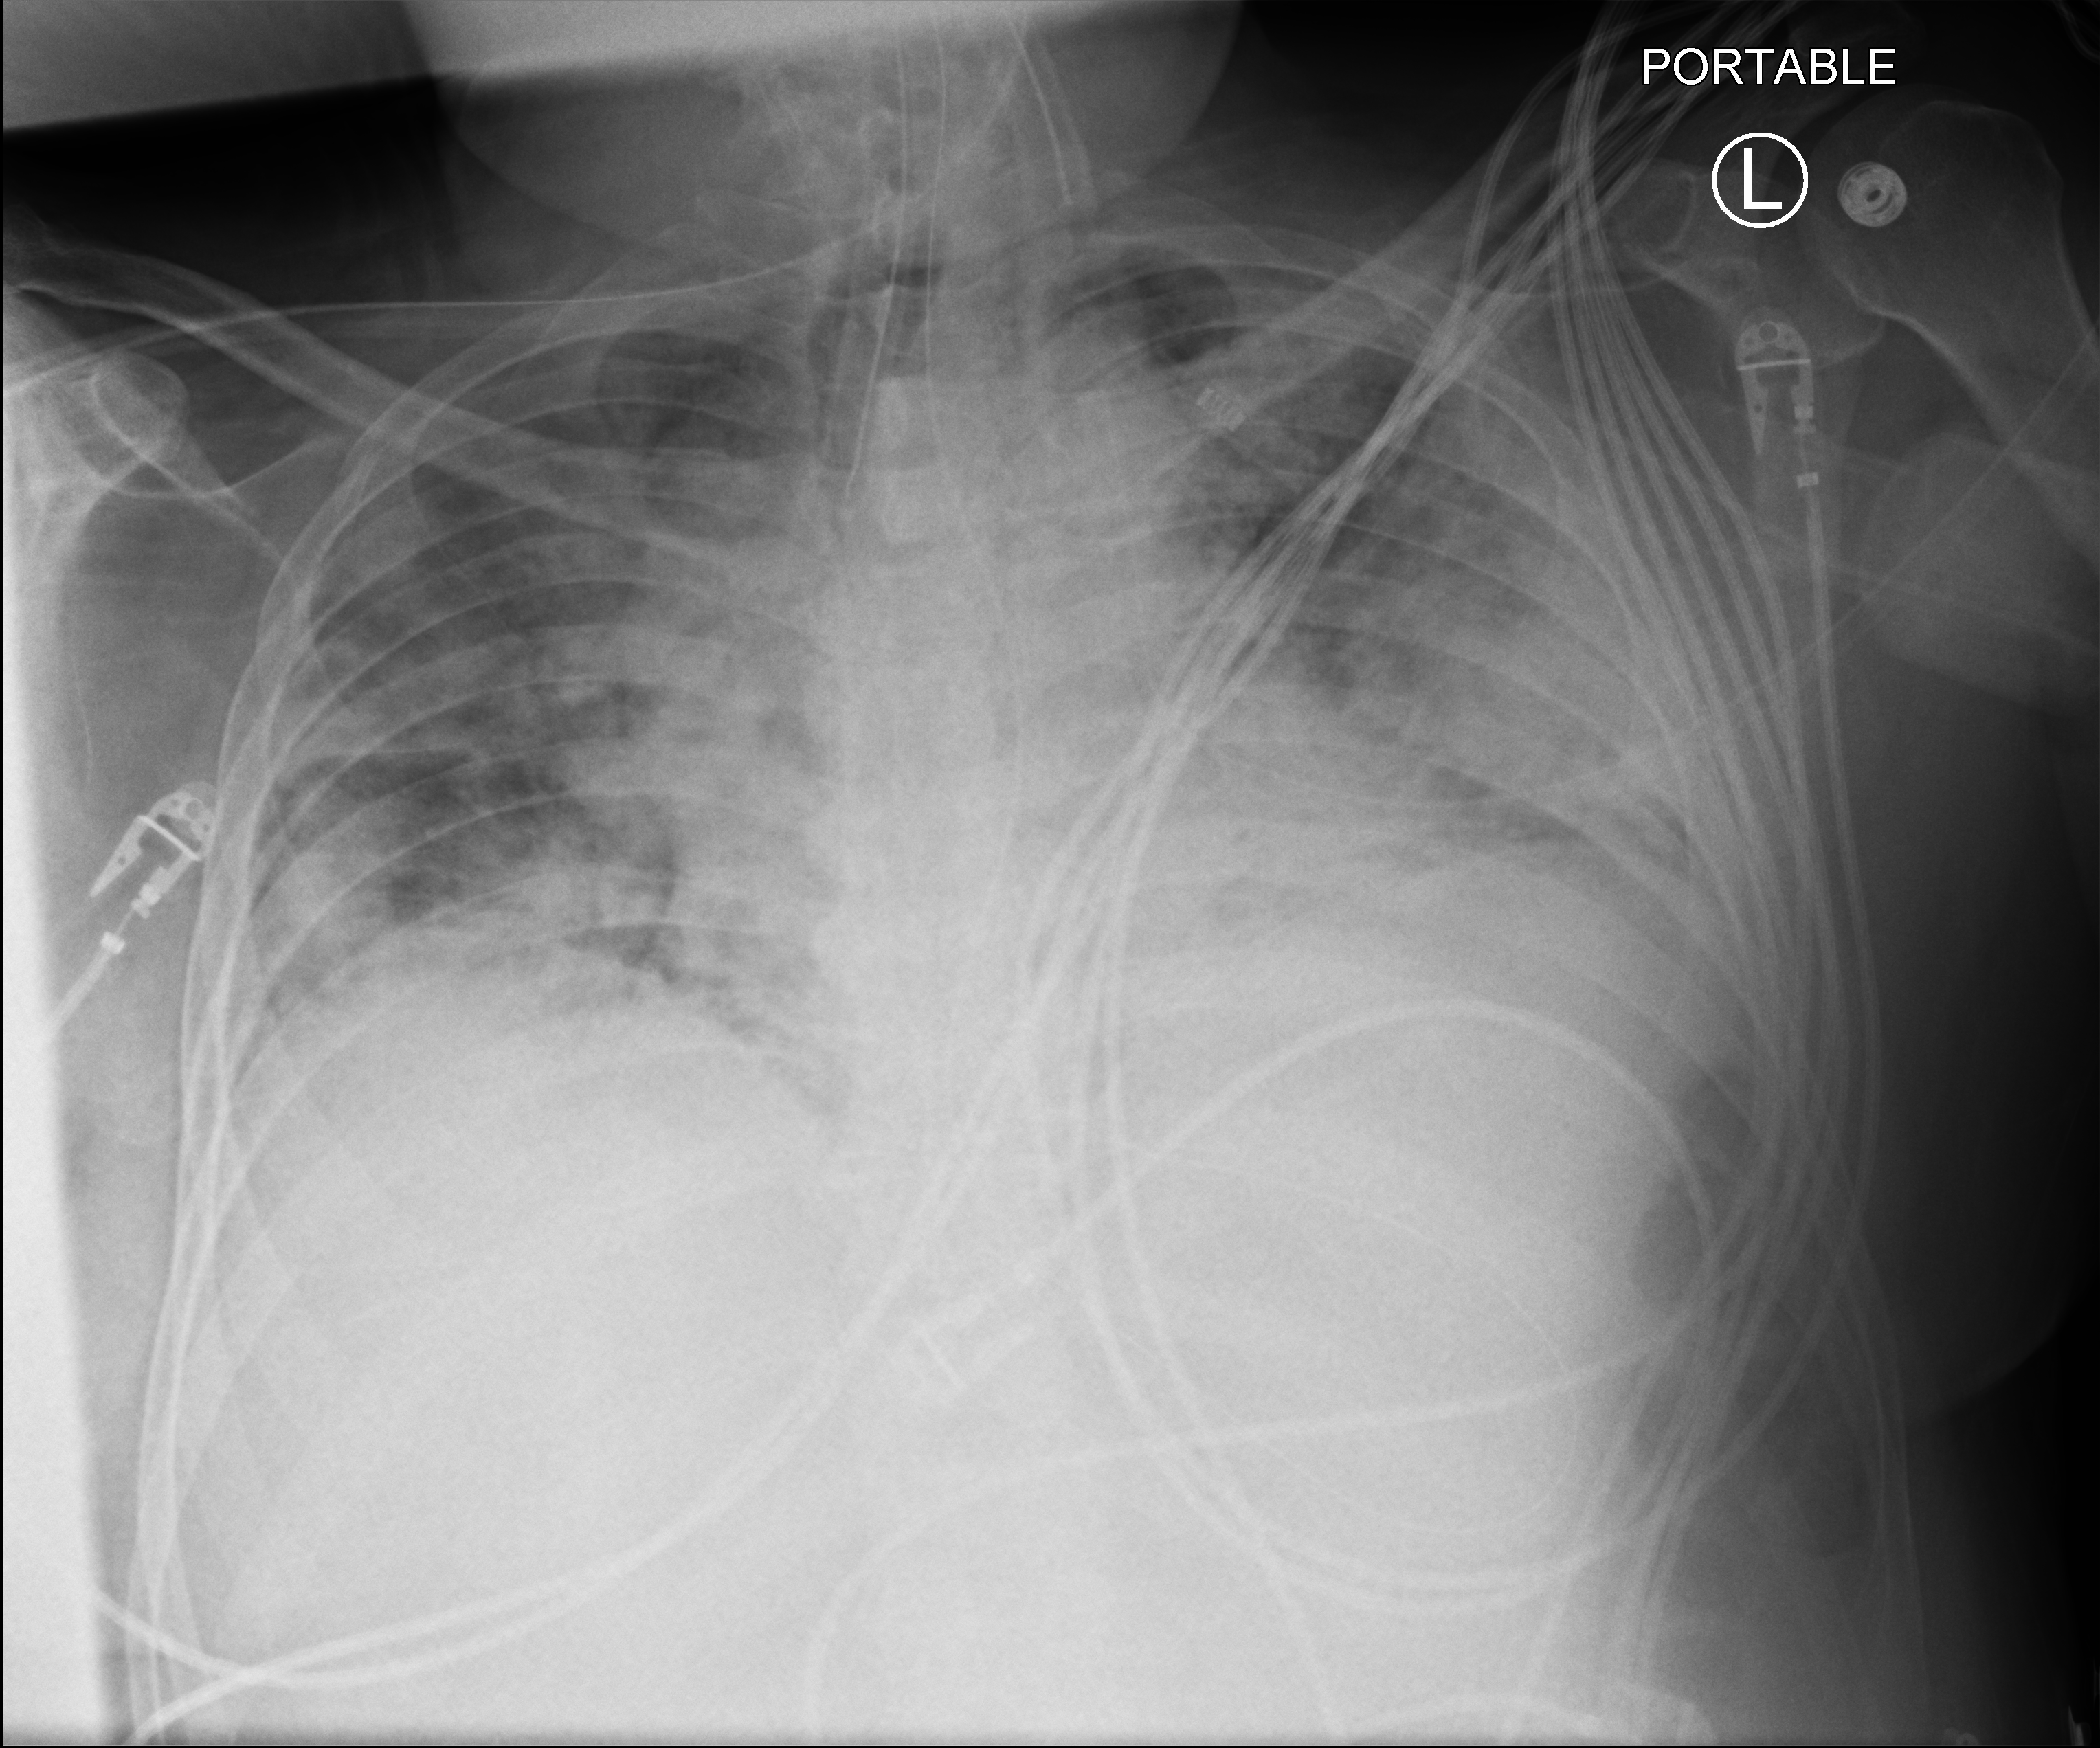
Chest X-ray (portable); anteroposterior (AP) projection. Patient hospitalised with COVID-19; male, aged 60–74 years.
Admission-level facts for this patient (not findings on this image; timing relative to this image not recorded): hypertension (admission record): yes; diabetes (admission record): no; admitted to intensive care during this hospital stay: yes.